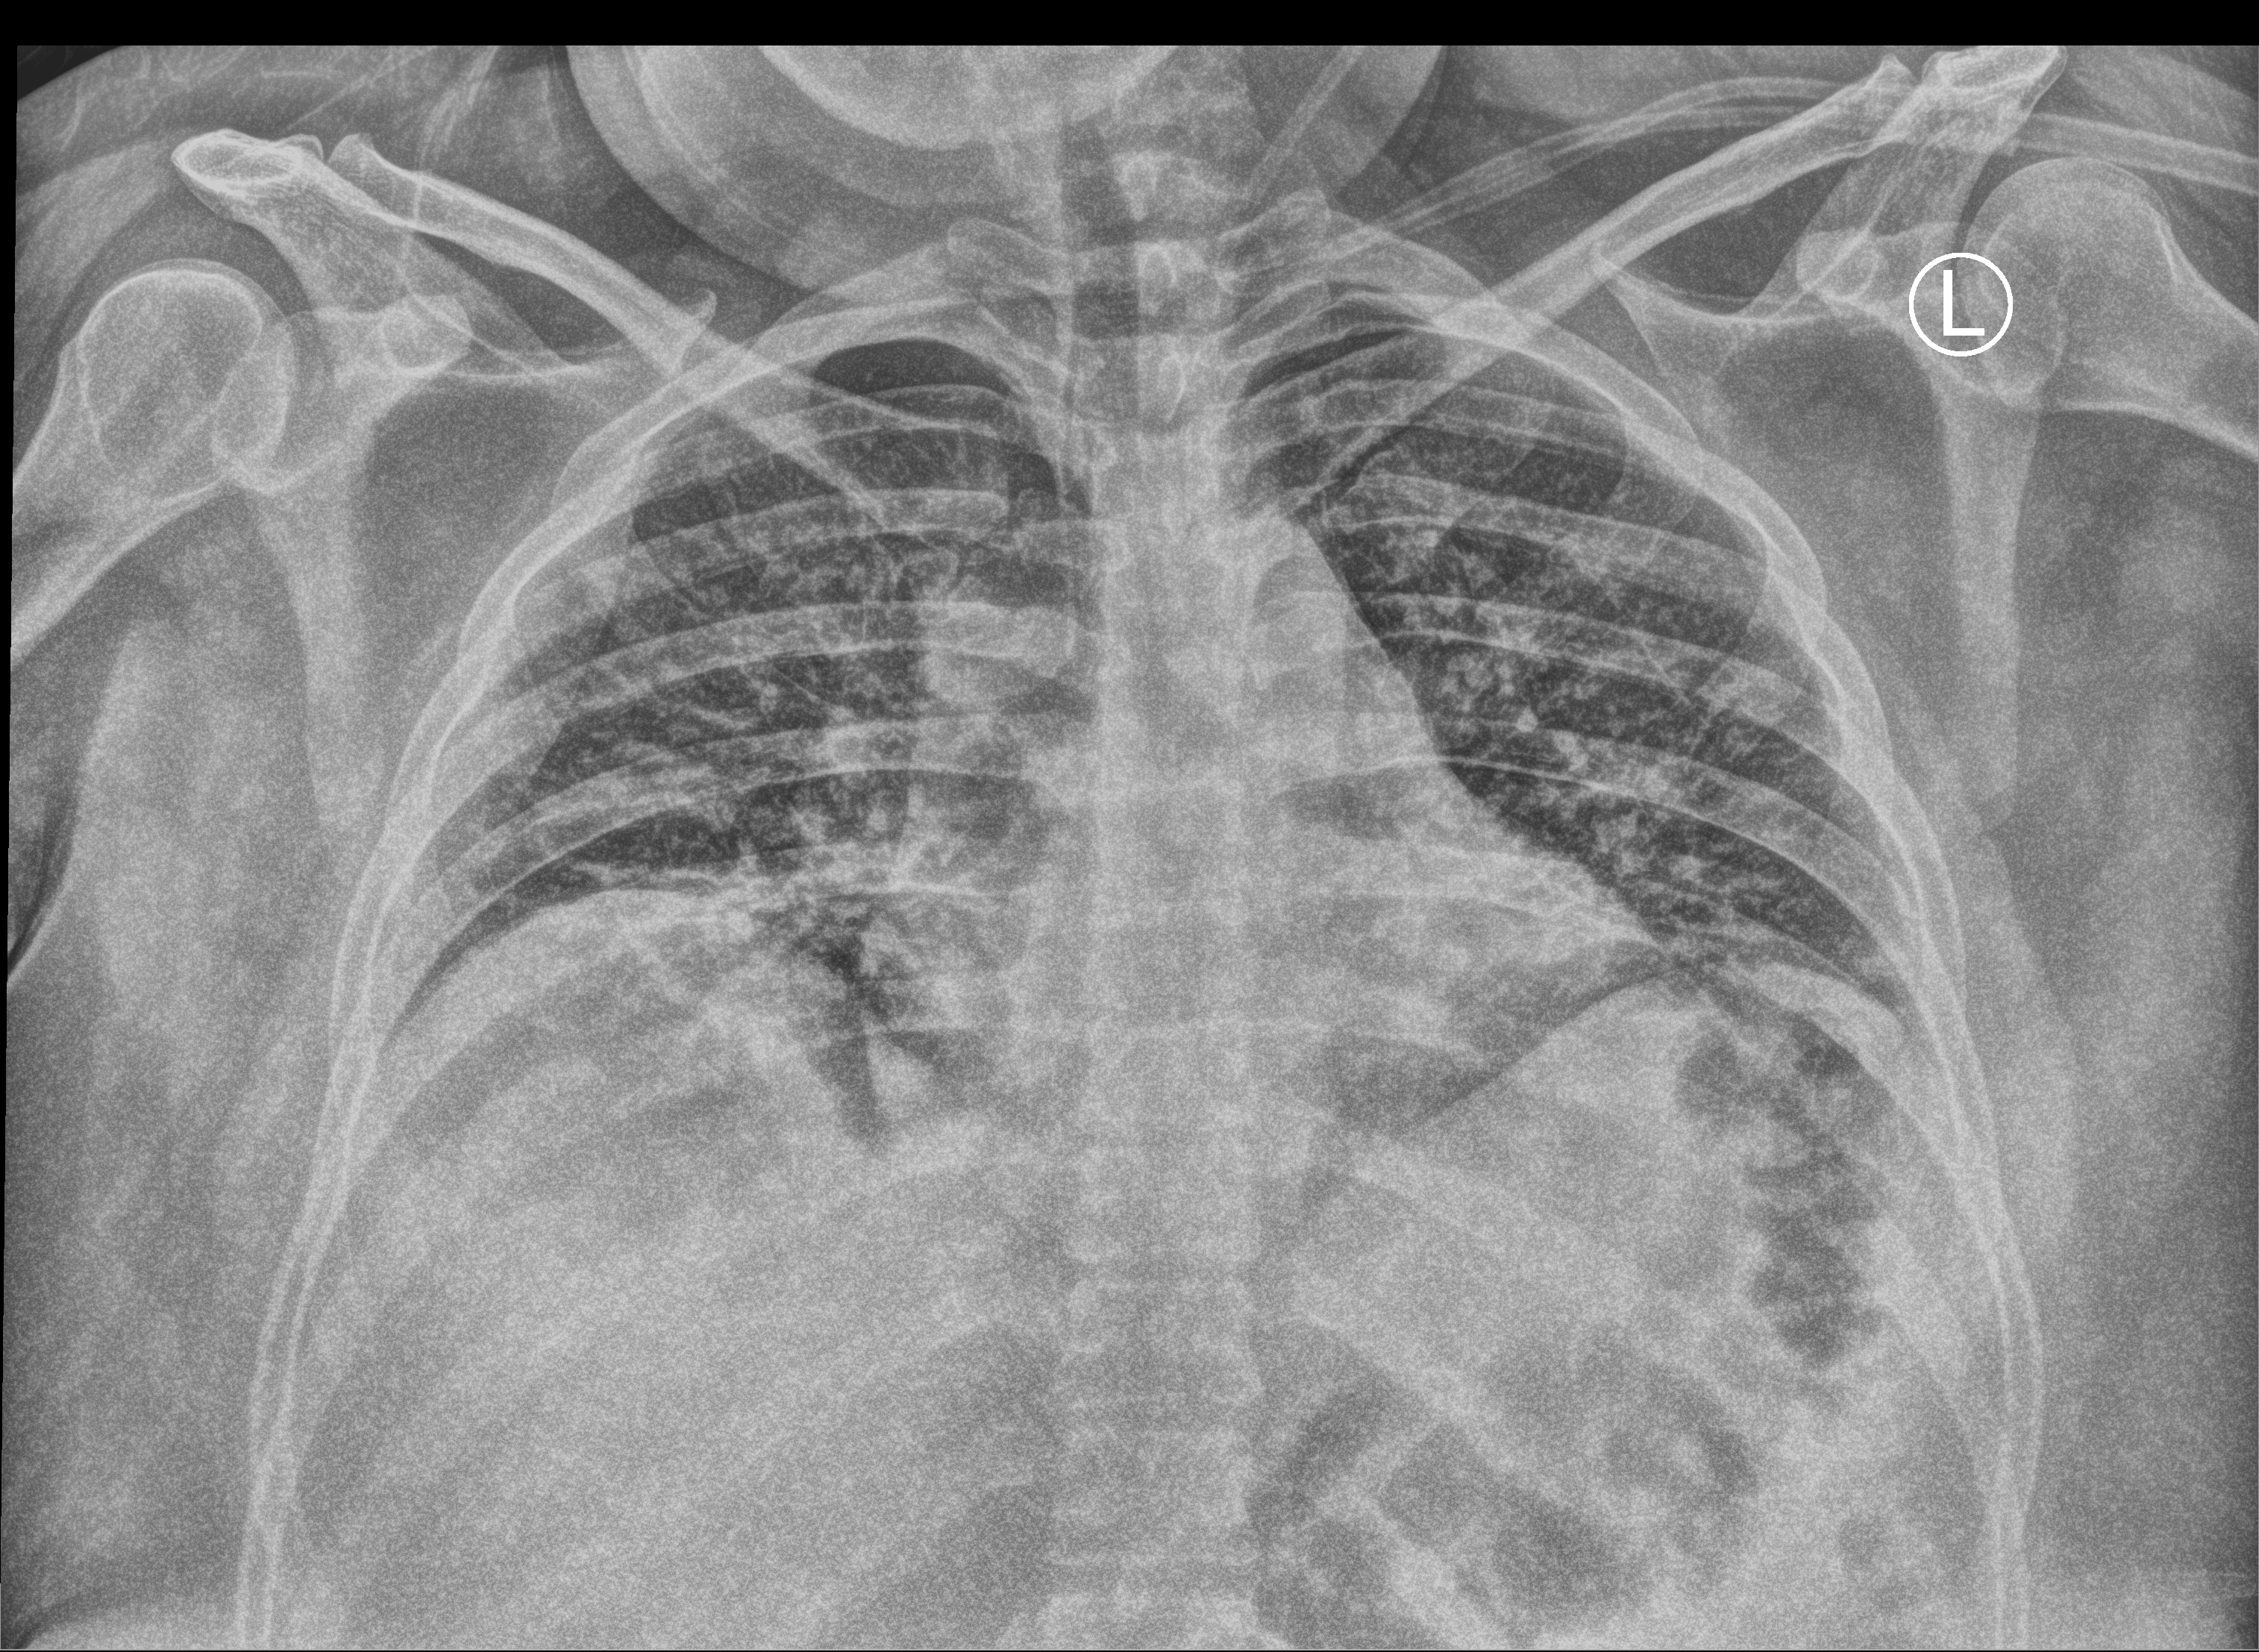
Bedside chest radiograph (computed radiography). Female patient hospitalised with COVID-19, age 18–59 years.
From the hospital-stay record, not from the radiograph (when in the stay this image was taken is not recorded):
- smoking status (admission record): never
- admitted to intensive care during this hospital stay: no
- mechanically ventilated during this hospital stay: no